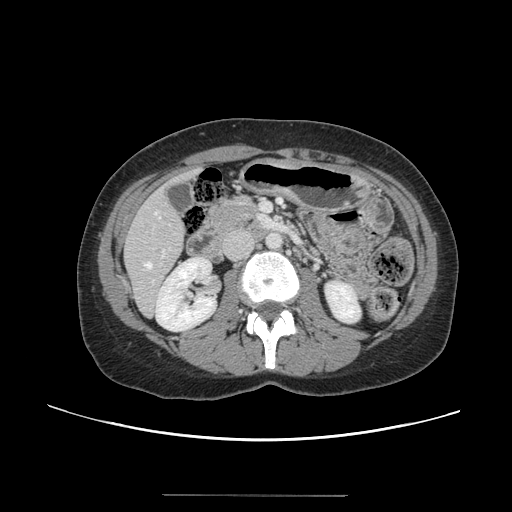
Contrast-enhanced abdominal CT, one axial slice. Position 50 of 144 along the scan axis. Soft-tissue window (W 400 / L 40 HU). 2.5 mm slice thickness. 512 × 512 image matrix, field of view 380 × 380 mm. Female patient, age 53 years. From the clinical record (not read from this slice): diagnosis: colorectal cancer liver metastases, imaged before liver resection; multiple liver metastases: yes.
Structures marked on this image (expert manual segmentation):
- hepatic veins: box from (x=146, y=212) to (x=160, y=268) px
- liver: (x=126, y=171)–(x=198, y=315)
- planned liver remnant (the part of the liver to remain after resection): (x=126, y=170)–(x=198, y=314)
- portal vein (with intrahepatic branches): (x=152, y=249)–(x=166, y=283)